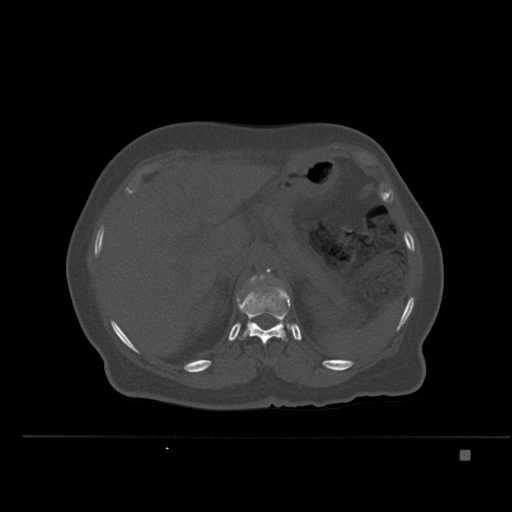
CT including the spine, one axial slice. Slice 252 of 477 in the series (ordered by position). Bone window (W 1800 / L 400 HU). 1.5 mm slice thickness. 512 × 512 image matrix, field of view 422 × 422 mm. Patient: female, 74 years. From the clinical record (not read from this slice): primary cancer: colon.
Annotated regions visible in this slice (semi-automatically segmented with operator editing):
- L1 vertebra: box from (x=238, y=275) to (x=274, y=297) px
- T12 vertebra: (x=236, y=283)–(x=292, y=344)